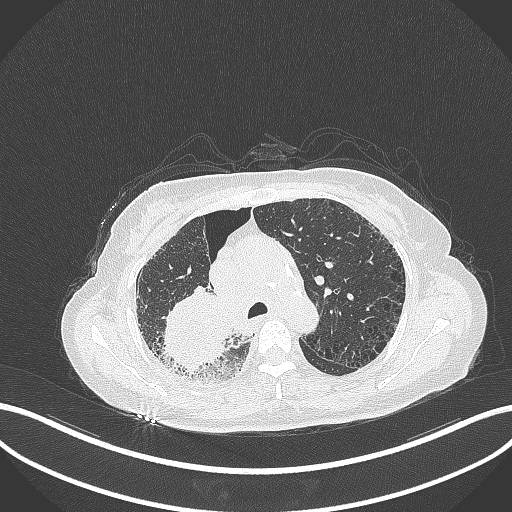
Chest CT, one axial slice. Position 238 of 408 along the scan axis. Reconstruction kernel B70f. 120 kVp. Lung window (W 1500 / L -600 HU). 1 mm slice thickness. 512 × 512 image matrix. Female patient, age 64 years. Case-level facts recorded for this patient, not image findings: clinical TNM (as recorded): T3 N3 M0.
Annotated regions visible in this slice (bounding box drawn by a radiologist):
- lung tumour (recorded histology: squamous cell carcinoma): bounding box <160,279,233,379> (left, top, right, bottom; pixels)